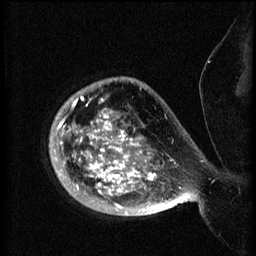
Breast MRI (dynamic contrast-enhanced), one sagittal slice. Slice 55 of 60 in the series (ordered by position). 3 images stored at this slice position (order not interpretable as contrast timing). 1.5 T. TE 4.2 ms, TR 8.2 ms. 2 mm slice thickness. 256 × 256 image matrix, field of view 200 × 200 mm. Female patient, age 50 years.
Structures marked on this image (semi-automatic segmentation, software-assisted and operator-edited):
- analysis volume of interest (the breast-tissue region the enhancement analysis was run in; not a lesion): bounding box (x1, y1, x2, y2) in pixels: (50, 78, 173, 217)
- tumour enhancement mask (voxels above the 70 % enhancement threshold inside the analysis volume of interest): (50, 96, 173, 215)